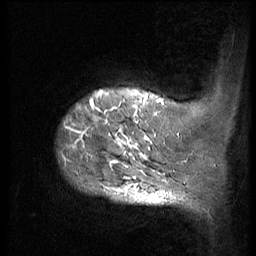
Breast MRI (dynamic contrast-enhanced), one sagittal slice; 3 images stored at this slice position (order not interpretable as contrast timing); 1.5 T; TE 4.2 ms, TR 9 ms; 2.5 mm slice thickness; 256 × 256 image matrix, field of view 180 × 180 mm. Patient: female, 49 years. Case-level facts recorded for this patient, not image findings: setting: breast cancer imaged before/during neoadjuvant chemotherapy; receptor status: HER2-positive.
Annotated regions visible in this slice (semi-automatically segmented with operator editing):
- analysis volume of interest (the breast-tissue region the enhancement analysis was run in; not a lesion): bounding box [x1, y1, x2, y2] px = [54, 85, 168, 207]
- tumour enhancement mask (voxels above the 140 % enhancement threshold inside the analysis volume of interest): [60, 90, 161, 199]